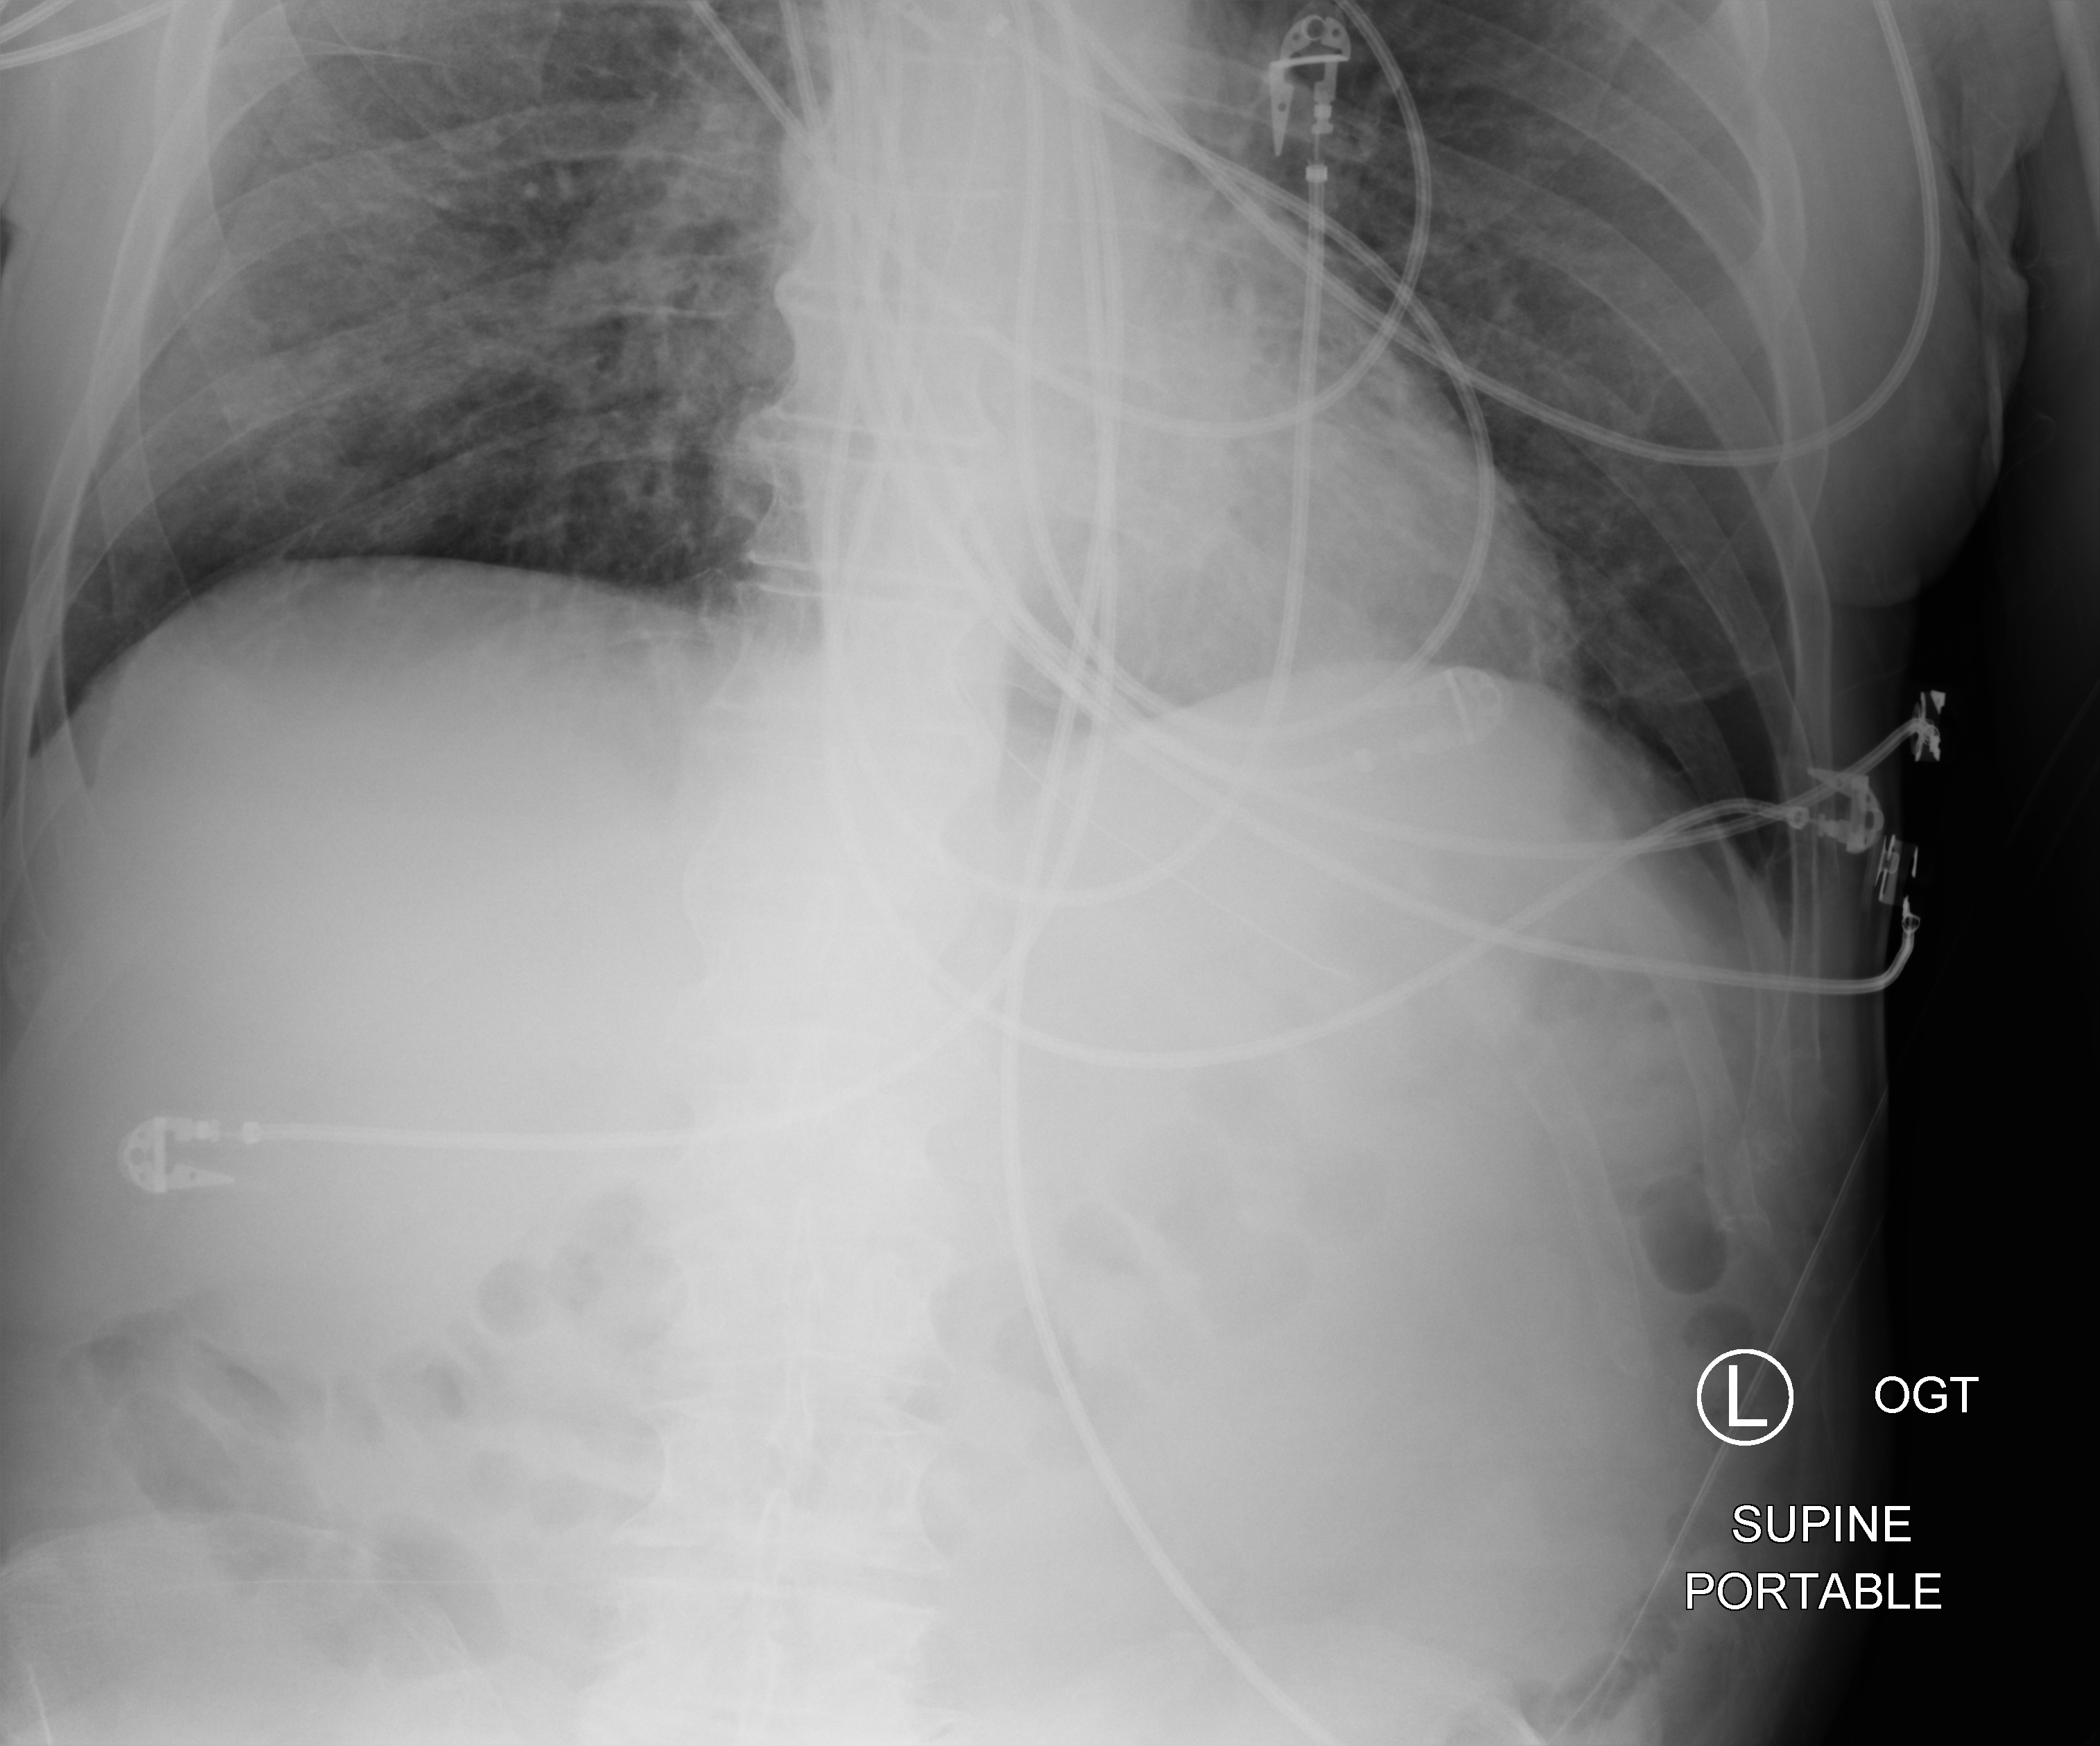
Chest X-ray (portable), anteroposterior (AP) projection. Patient hospitalised with COVID-19; male, aged 60–74 years.
Admission-level facts for this patient (not findings on this image; timing relative to this image not recorded): mechanically ventilated during this hospital stay: yes; admitted to intensive care during this hospital stay: yes; hypertension (admission record): yes.